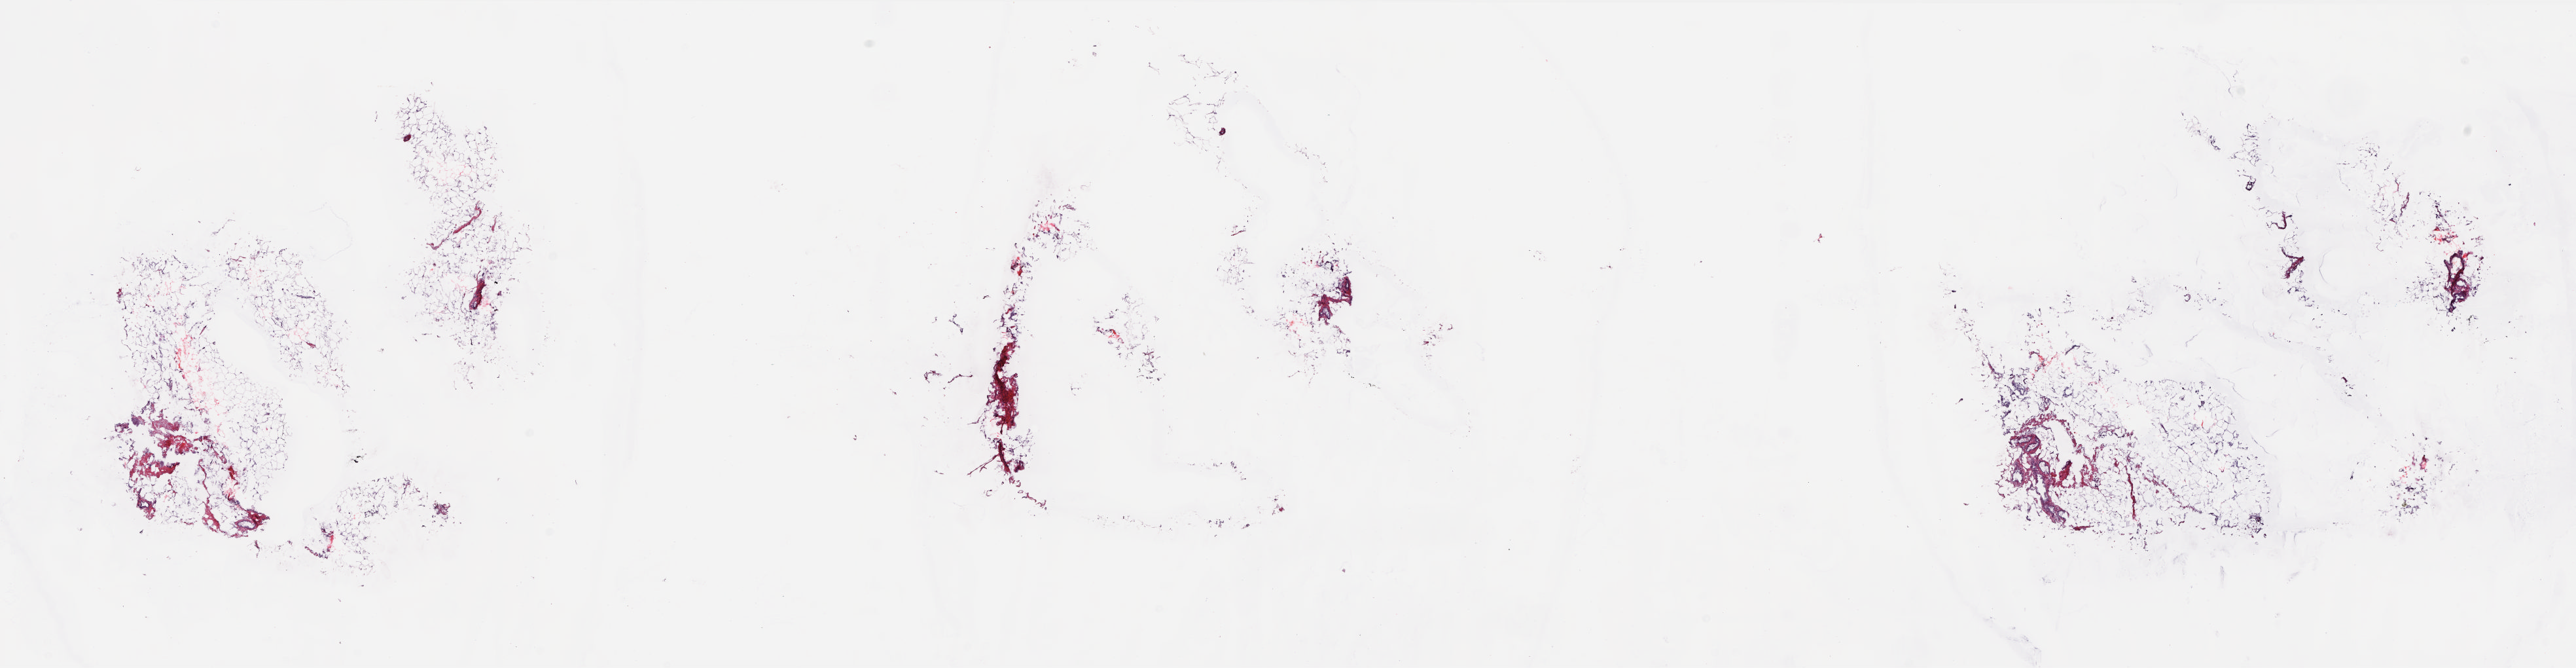
Whole-slide histology image, Hematoxylin and eosin (H&E) stained, low-resolution overview of the scanned area, about 31.7 x 8.2 mm (from a 20x scan). Frozen section from the top of the tissue portion. Solid tissue normal (non-tumour tissue) sample from the breast. Patient: female, age at initial diagnosis 54 years. Composition of this section per pathologist review: tumour cells 0%, tumour nuclei 0%, normal cells 3%, stromal cells 97%, necrosis 0%. Inflammatory infiltration, as recorded: lymphocyte infiltration 1%, monocyte infiltration 0%, neutrophil infiltration 0%.
- this section: solid tissue normal (non-tumour) sample from the same patient
- patient diagnosis: Infiltrating duct carcinoma, NOS